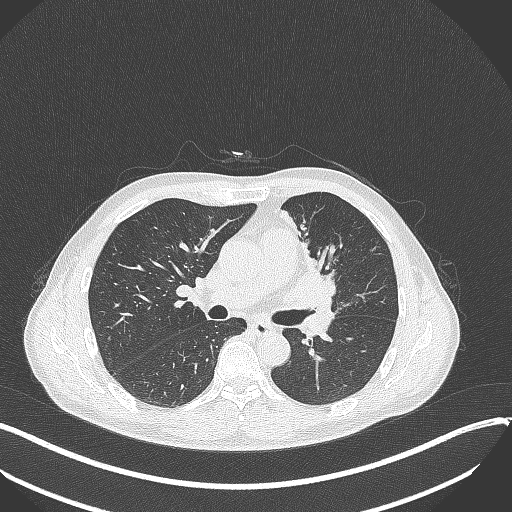
Chest CT, one axial slice. Position 192 of 411 along the scan axis. Reconstruction kernel B70f. 120 kVp. Lung window (W 1500 / L -600 HU). 1 mm slice thickness. 512 × 512 image matrix, field of view 400 × 400 mm. Male patient, age 56 years. Case-level facts recorded for this patient, not image findings: clinical TNM (as recorded): T2a N0 M0.
Annotated regions visible in this slice (rectangle marked by the reading radiologist):
- lung tumour (recorded histology: squamous cell carcinoma): box from (x=277, y=257) to (x=352, y=310) px